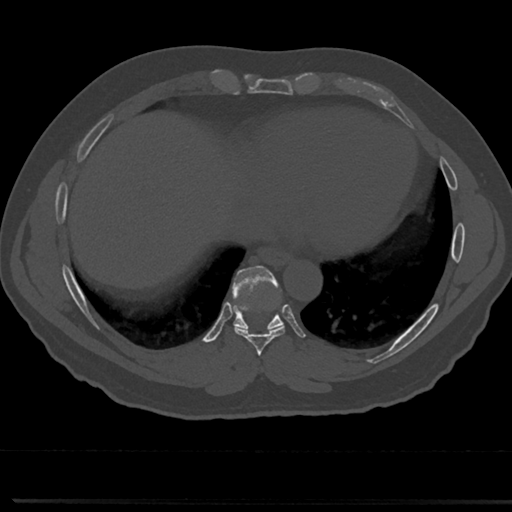
CT including the spine, one axial slice; 120 kVp; bone window (W 1800 / L 400 HU); 0.5 mm slice thickness; 512 × 512 image matrix, field of view 355 × 355 mm. Male patient, age 61 years. Case-level facts recorded for this patient, not image findings: primary cancer: prostate.
Outlined on this slice (semi-automatic segmentation, software-assisted and operator-edited):
- T7 vertebra: bounding box [x1, y1, x2, y2] px = [259, 346, 266, 377]
- T8 vertebra: [211, 271, 309, 356]